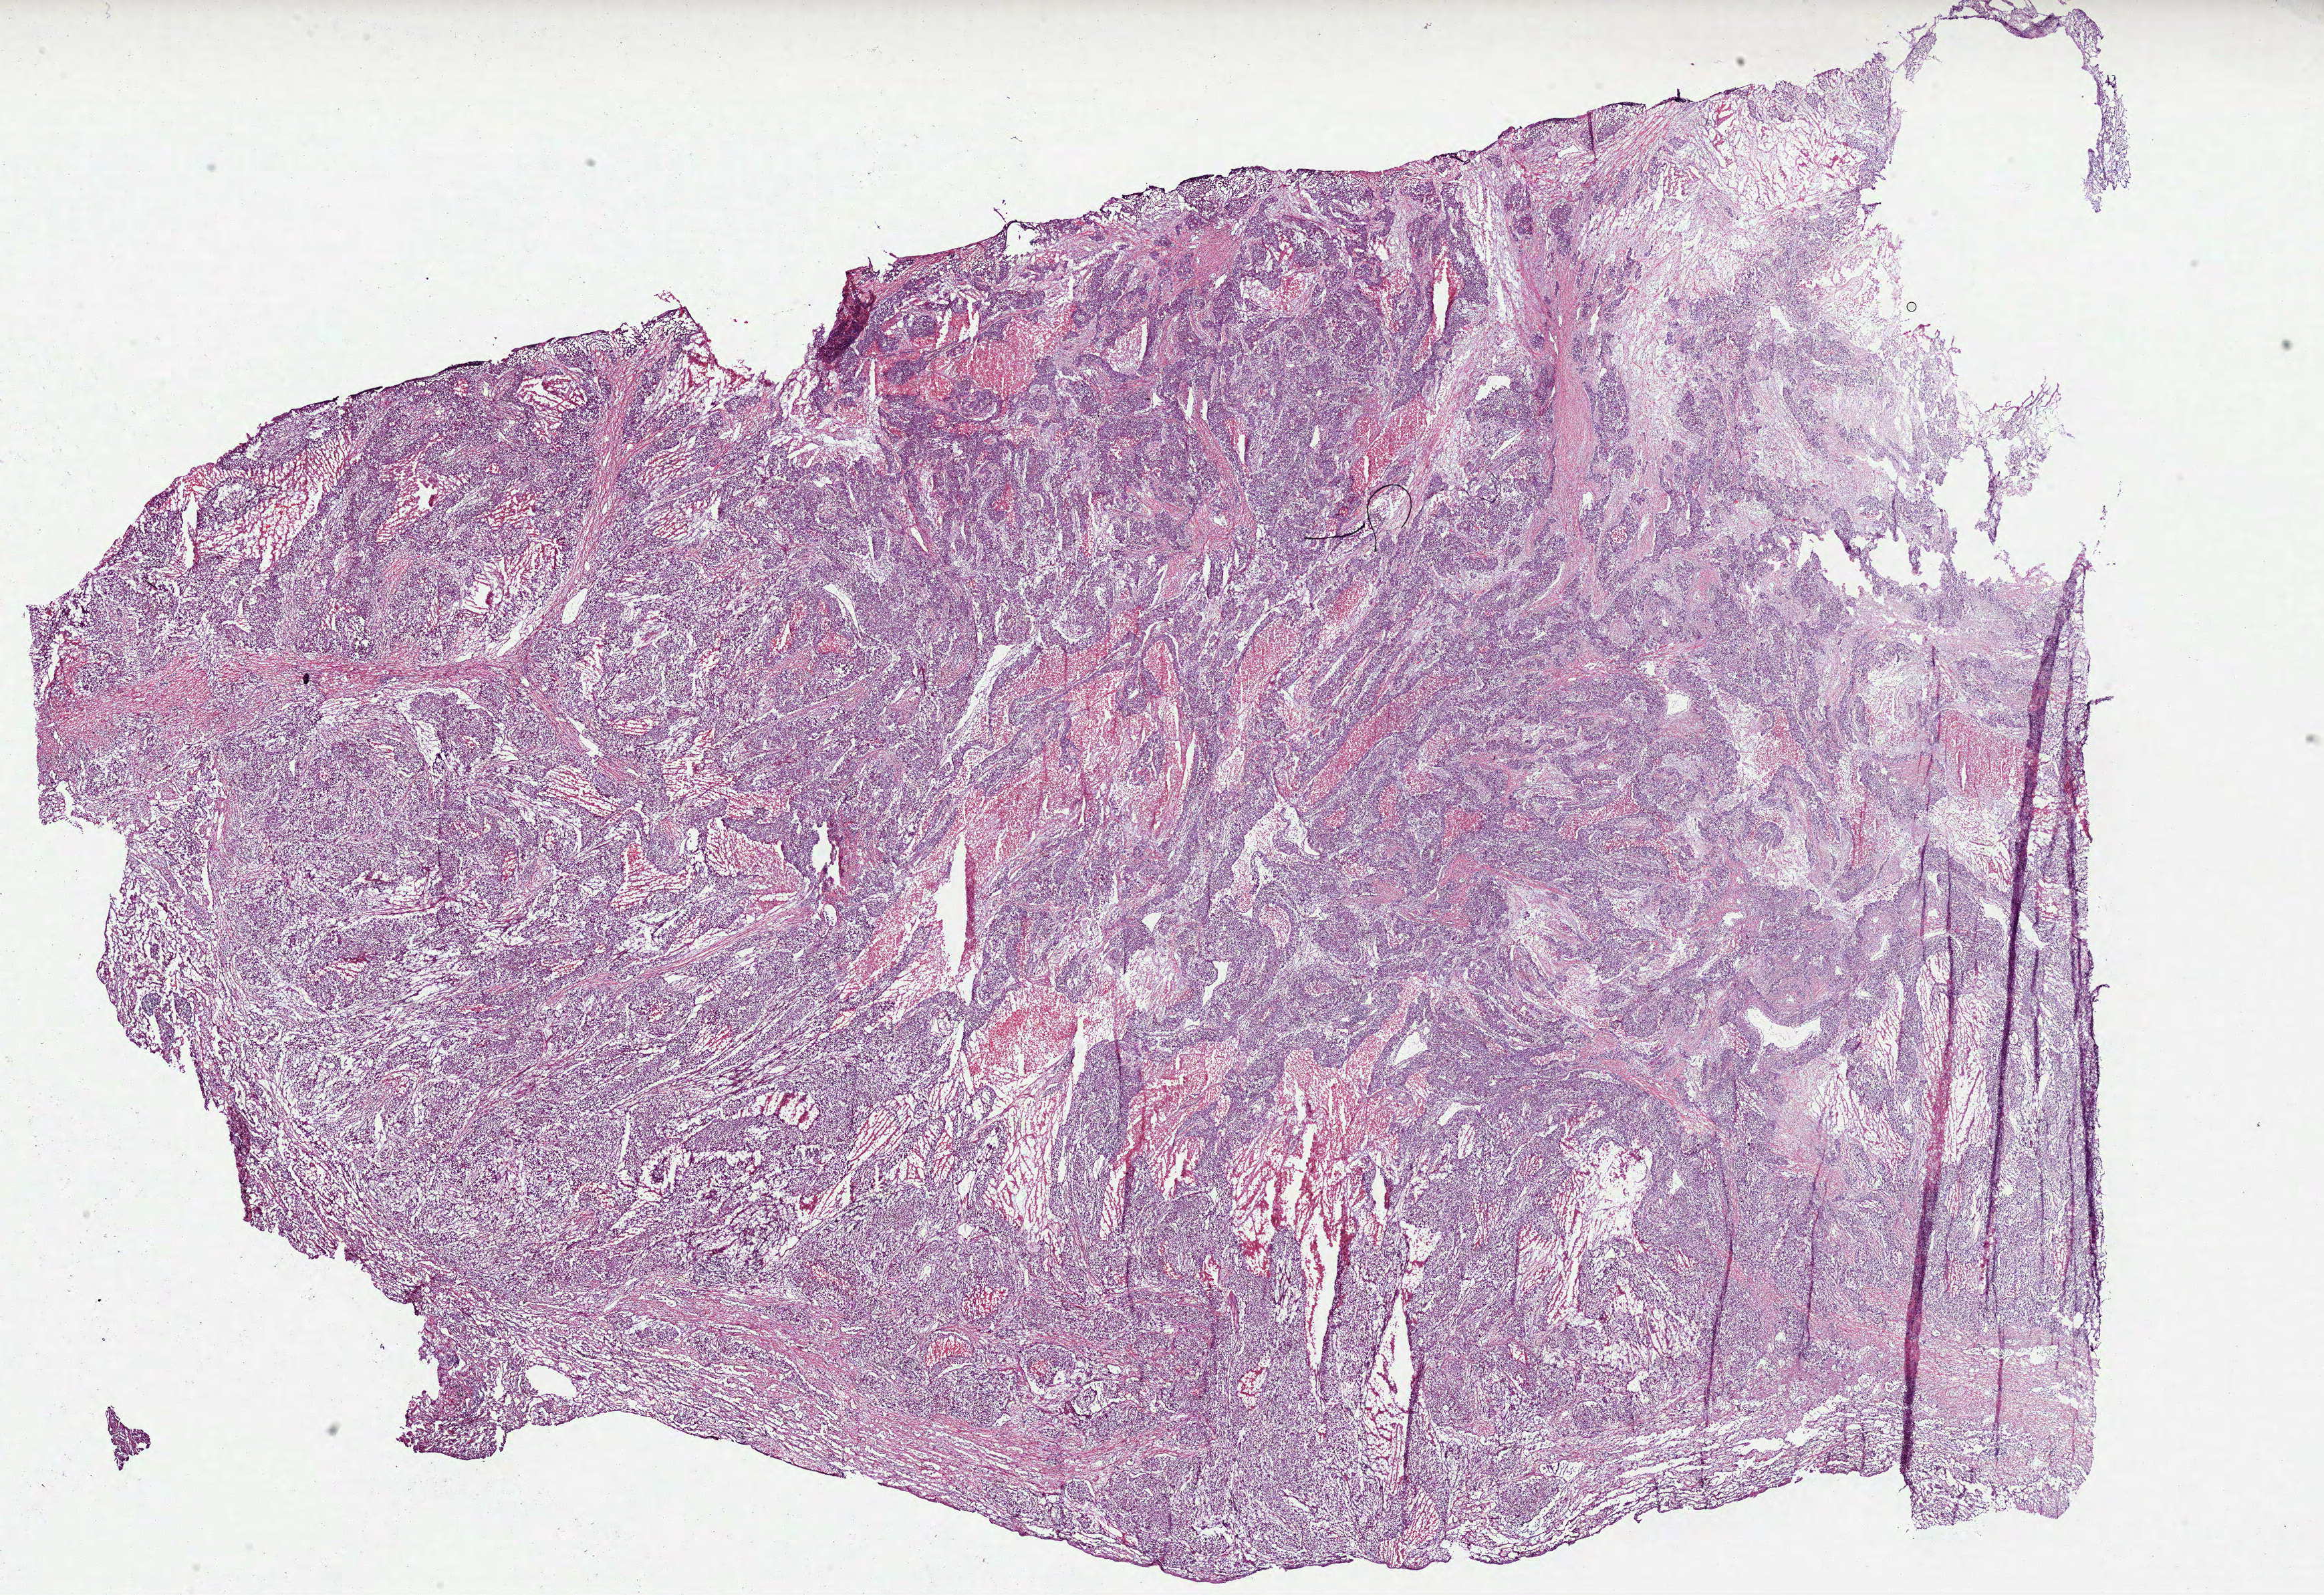
Digitized Hematoxylin and eosin (H&E) stained tissue section (whole slide) — shown as a low-resolution overview of the whole scanned area (about 28.0 x 19.2 mm, slide scanned at 40x), frozen section from the bottom of the tissue portion, lung, primary tumour sample. Male patient; age at initial diagnosis 46 years. Pathologist review of this section (percent, as recorded): tumour cells 72%, tumour nuclei 75%, normal cells 0%, stromal cells 10%, necrosis 18%.
AJCC pathologic stage: IB. Histologic diagnosis: Squamous cell carcinoma, NOS (upper lobe, lung).